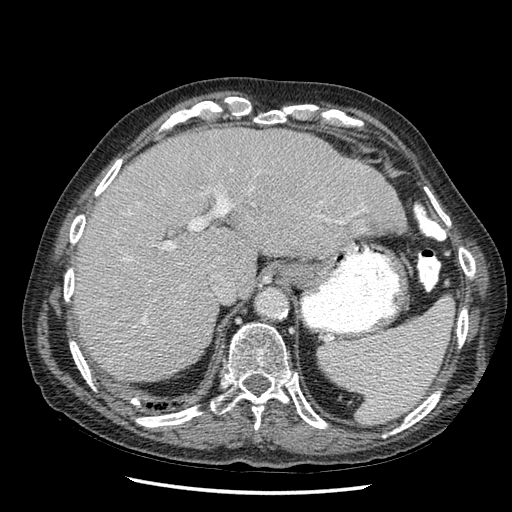
Contrast-enhanced abdominal CT (liver protocol), one axial slice. Slice 40 of 67 in the series (ordered by position). Reconstruction kernel STANDARD. 120 kVp. Soft-tissue window (W 400 / L 40 HU). 2.5 mm slice thickness. 512 × 512 image matrix, field of view 360 × 360 mm. From the clinical record (not read from this slice): diagnosis: hepatocellular carcinoma (patient treated with transarterial chemoembolisation; whether this scan precedes or follows treatment is not stated here); TNM stage (as recorded): Stage-I; Child-Pugh class: A; tumour differentiation: moderately differentiated; tumour nodularity: uninodular.
Outlined on this slice (semi-automatic segmentation, software-assisted and operator-edited):
- liver parenchyma outside the tumour (the mass and vessels are separate outlines, so this box may not span the whole liver): bounding box <72,126,406,382> (left, top, right, bottom; pixels)
- liver vessels: <133,171,348,356>